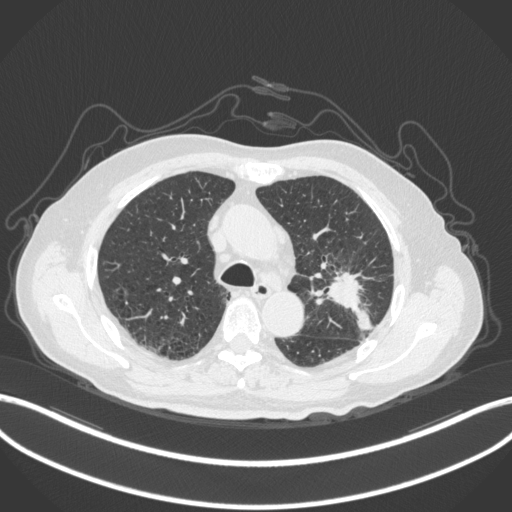
Chest CT, one axial slice. Position 197 of 331 along the scan axis. Lung window (W 1500 / L -600 HU). 512 × 512 image matrix, field of view 400 × 400 mm. Patient: male, 79 years. From the clinical record (not read from this slice): clinical TNM (as recorded): T2a N1 M1; histopathological grade: G3.
Outlined on this slice (bounding box drawn by a radiologist):
- lung tumour (recorded histology: adenocarcinoma): bounding box (x1, y1, x2, y2) in pixels: (308, 258, 376, 336)